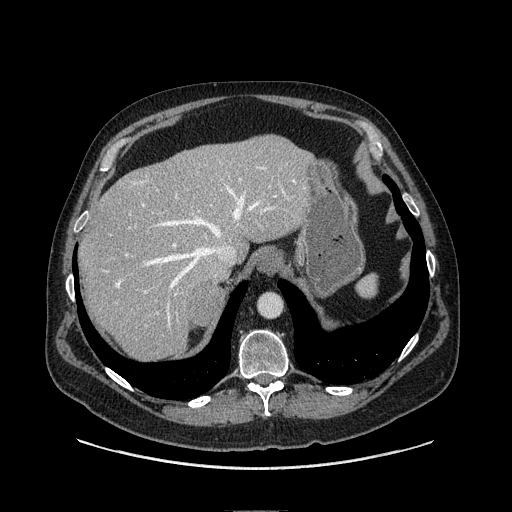
Contrast-enhanced abdominal CT, one axial slice. Slice 91 of 149 in the series (ordered by position). Soft-tissue window (W 400 / L 40 HU). 1.25 mm slice thickness. 512 × 512 image matrix, field of view 440 × 440 mm. Male patient. From the clinical record (not read from this slice): diagnosis: adrenocortical carcinoma; tumour side: right adrenal; tumour size at pathology: 7.5 cm; Ki-67 index: 15 %.
Structures marked on this image (semi-automatic segmentation, software-assisted and operator-edited):
- mass: box from (x=191, y=283) to (x=221, y=327) px